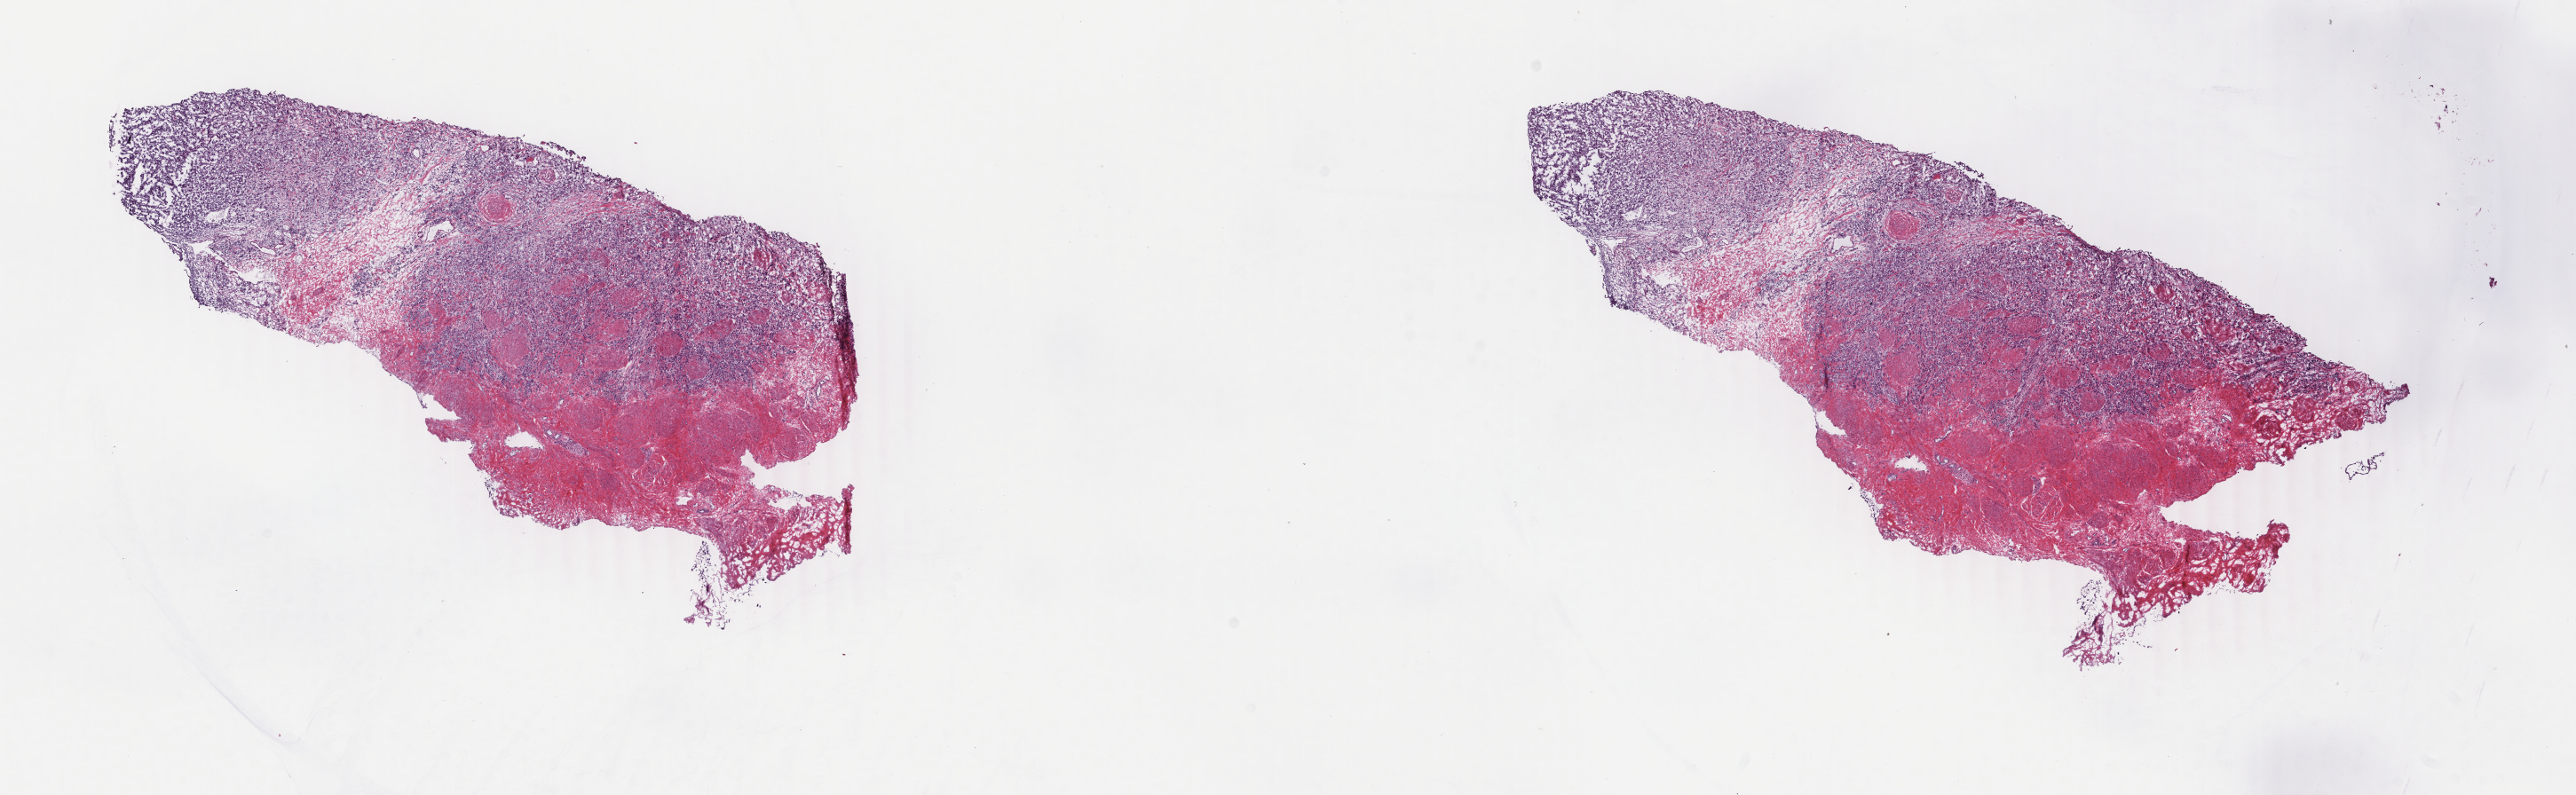
Digitized H&E tissue section (whole slide) — whole scanned area (about 23.1 x 7.1 mm, slide scanned at 40x) shown as a low-resolution overview. Frozen section from the top of the tissue portion. Bladder, primary tumour sample. Male, age 60 years at initial diagnosis. Histologic grade: high grade. Composition of this section per pathologist review: tumour cells 70%, tumour nuclei 70%, normal cells 0%, stromal cells 30%, necrosis 0%. Inflammatory infiltration, as recorded: lymphocyte infiltration 5%, monocyte infiltration 0%, neutrophil infiltration 0%.
• pathologic diagnosis: Transitional cell carcinoma
• AJCC pathologic stage: IV (6th edition)